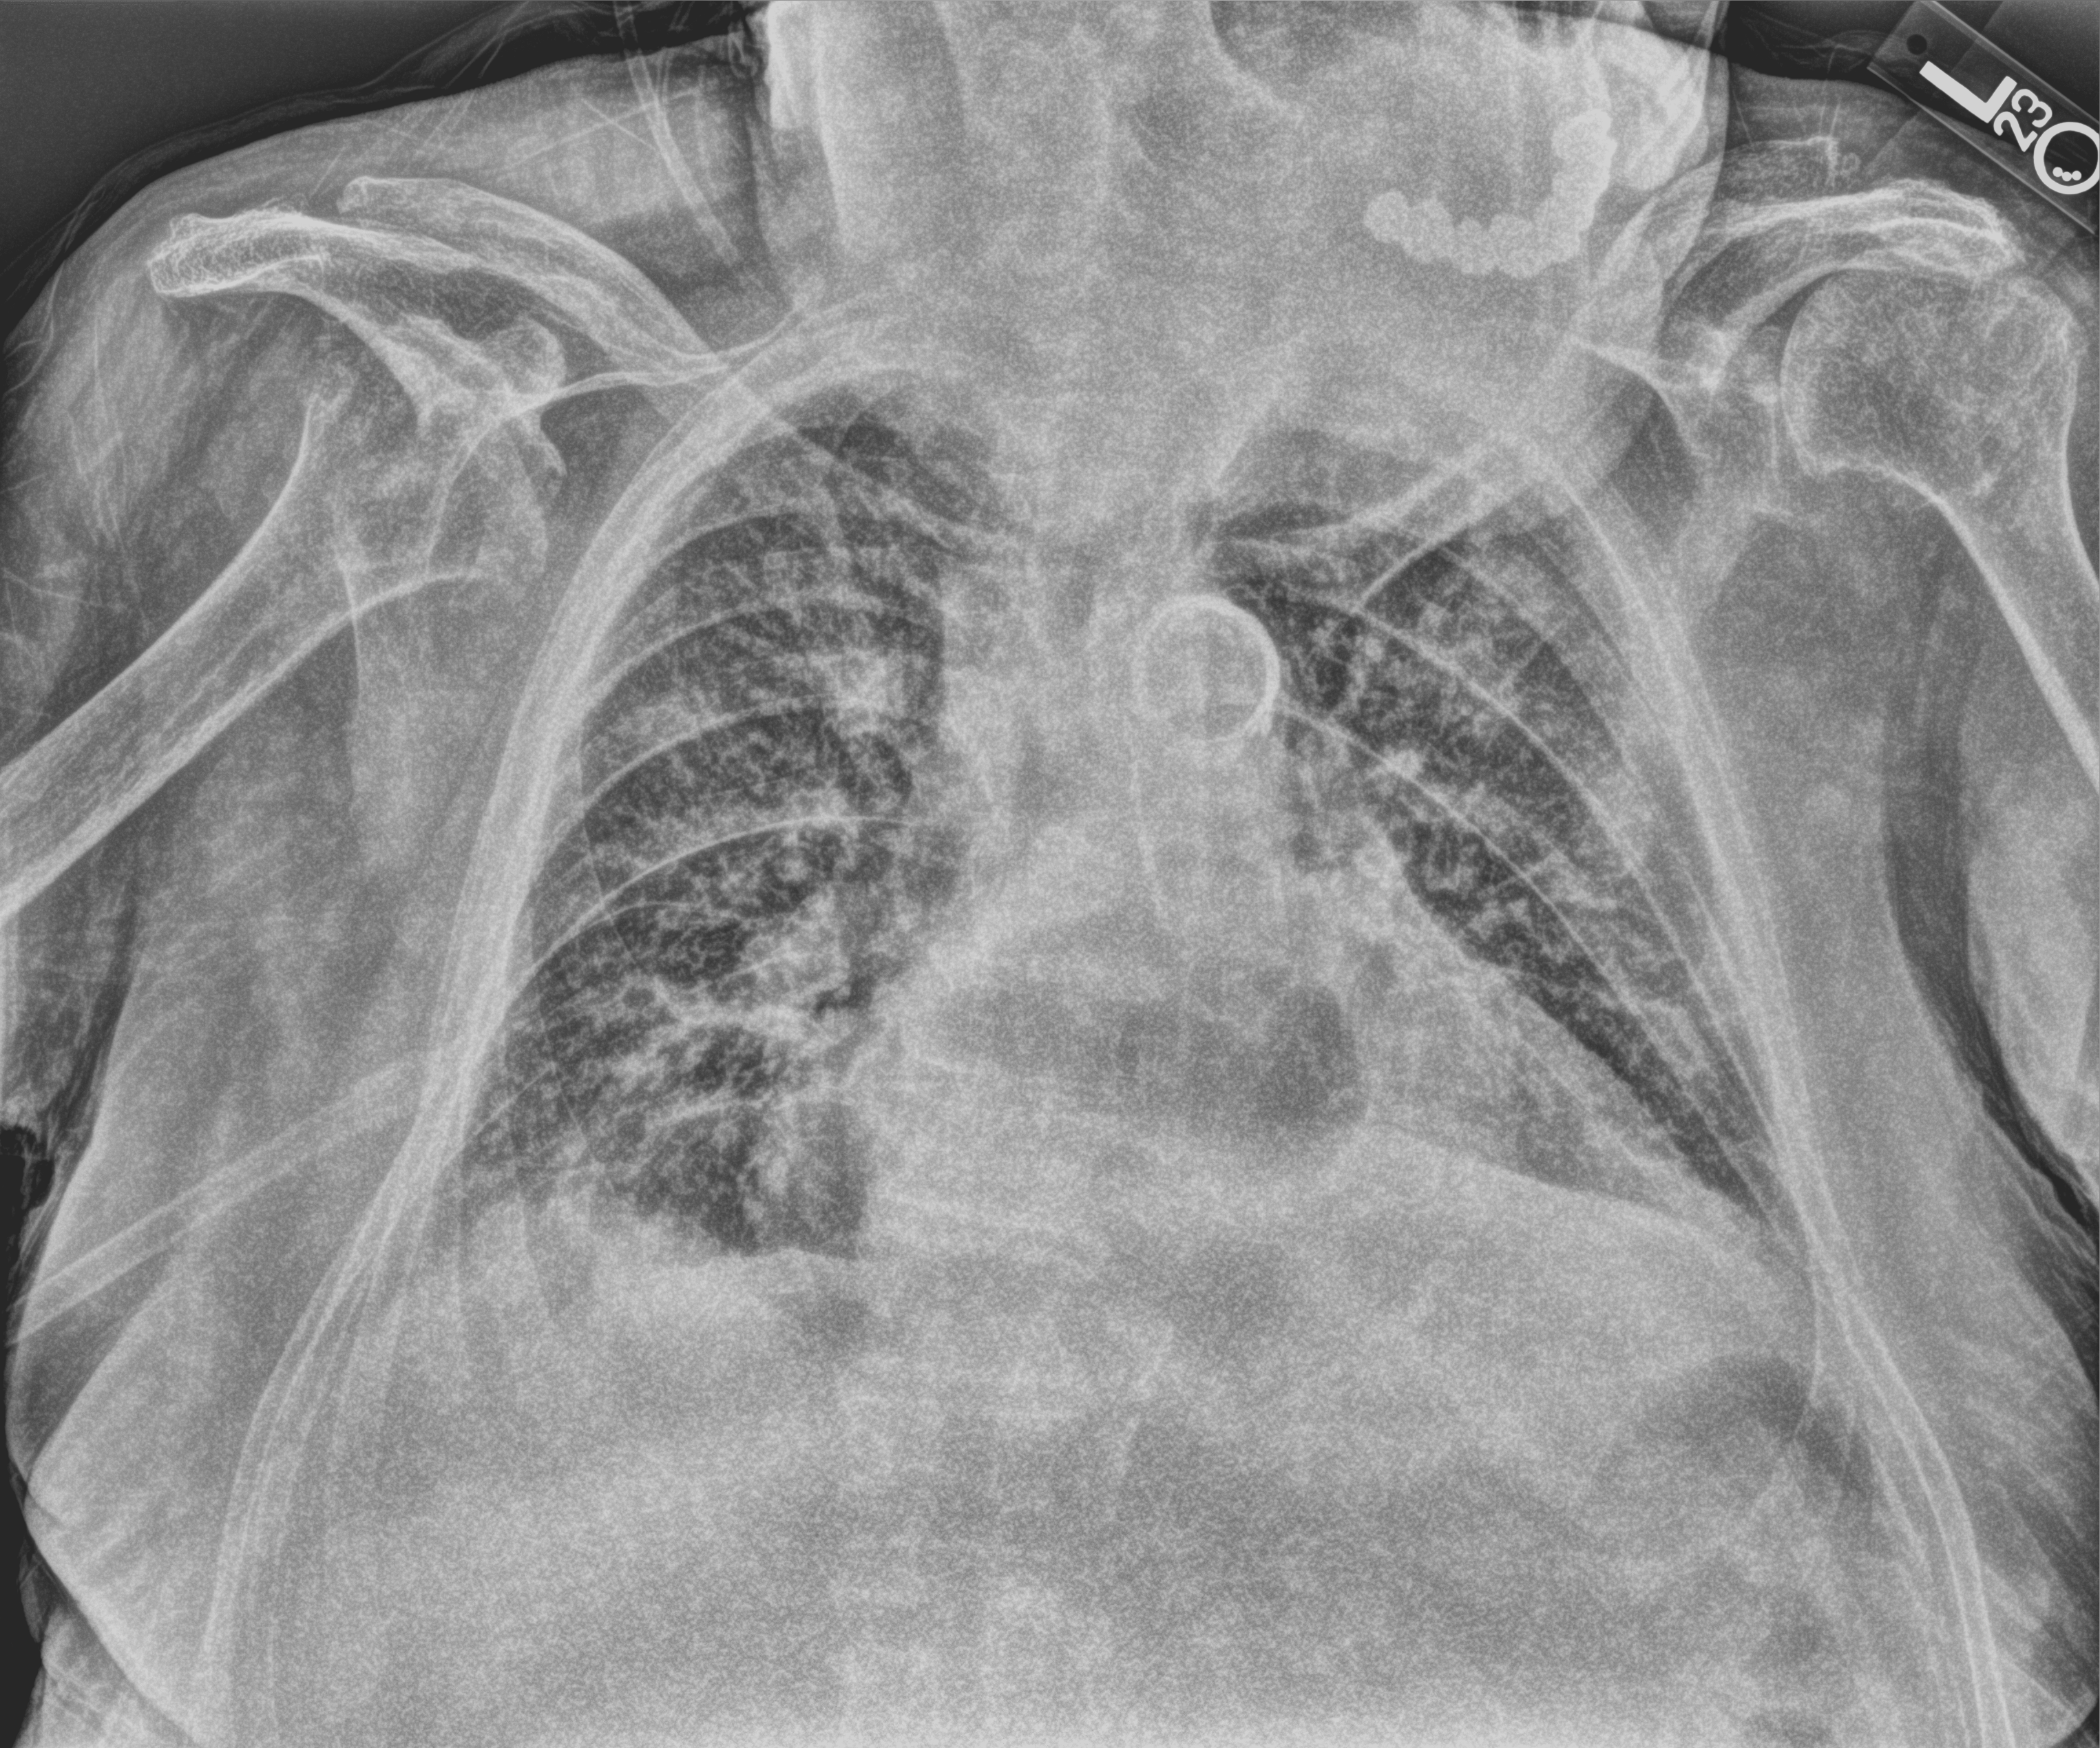
Chest X-ray (portable). Patient hospitalised with COVID-19; male, aged 75–90 years.
Hospital-stay facts (about this admission, not read from this image; timing relative to this image not recorded): diabetes (admission record): yes; COPD (admission record): no.